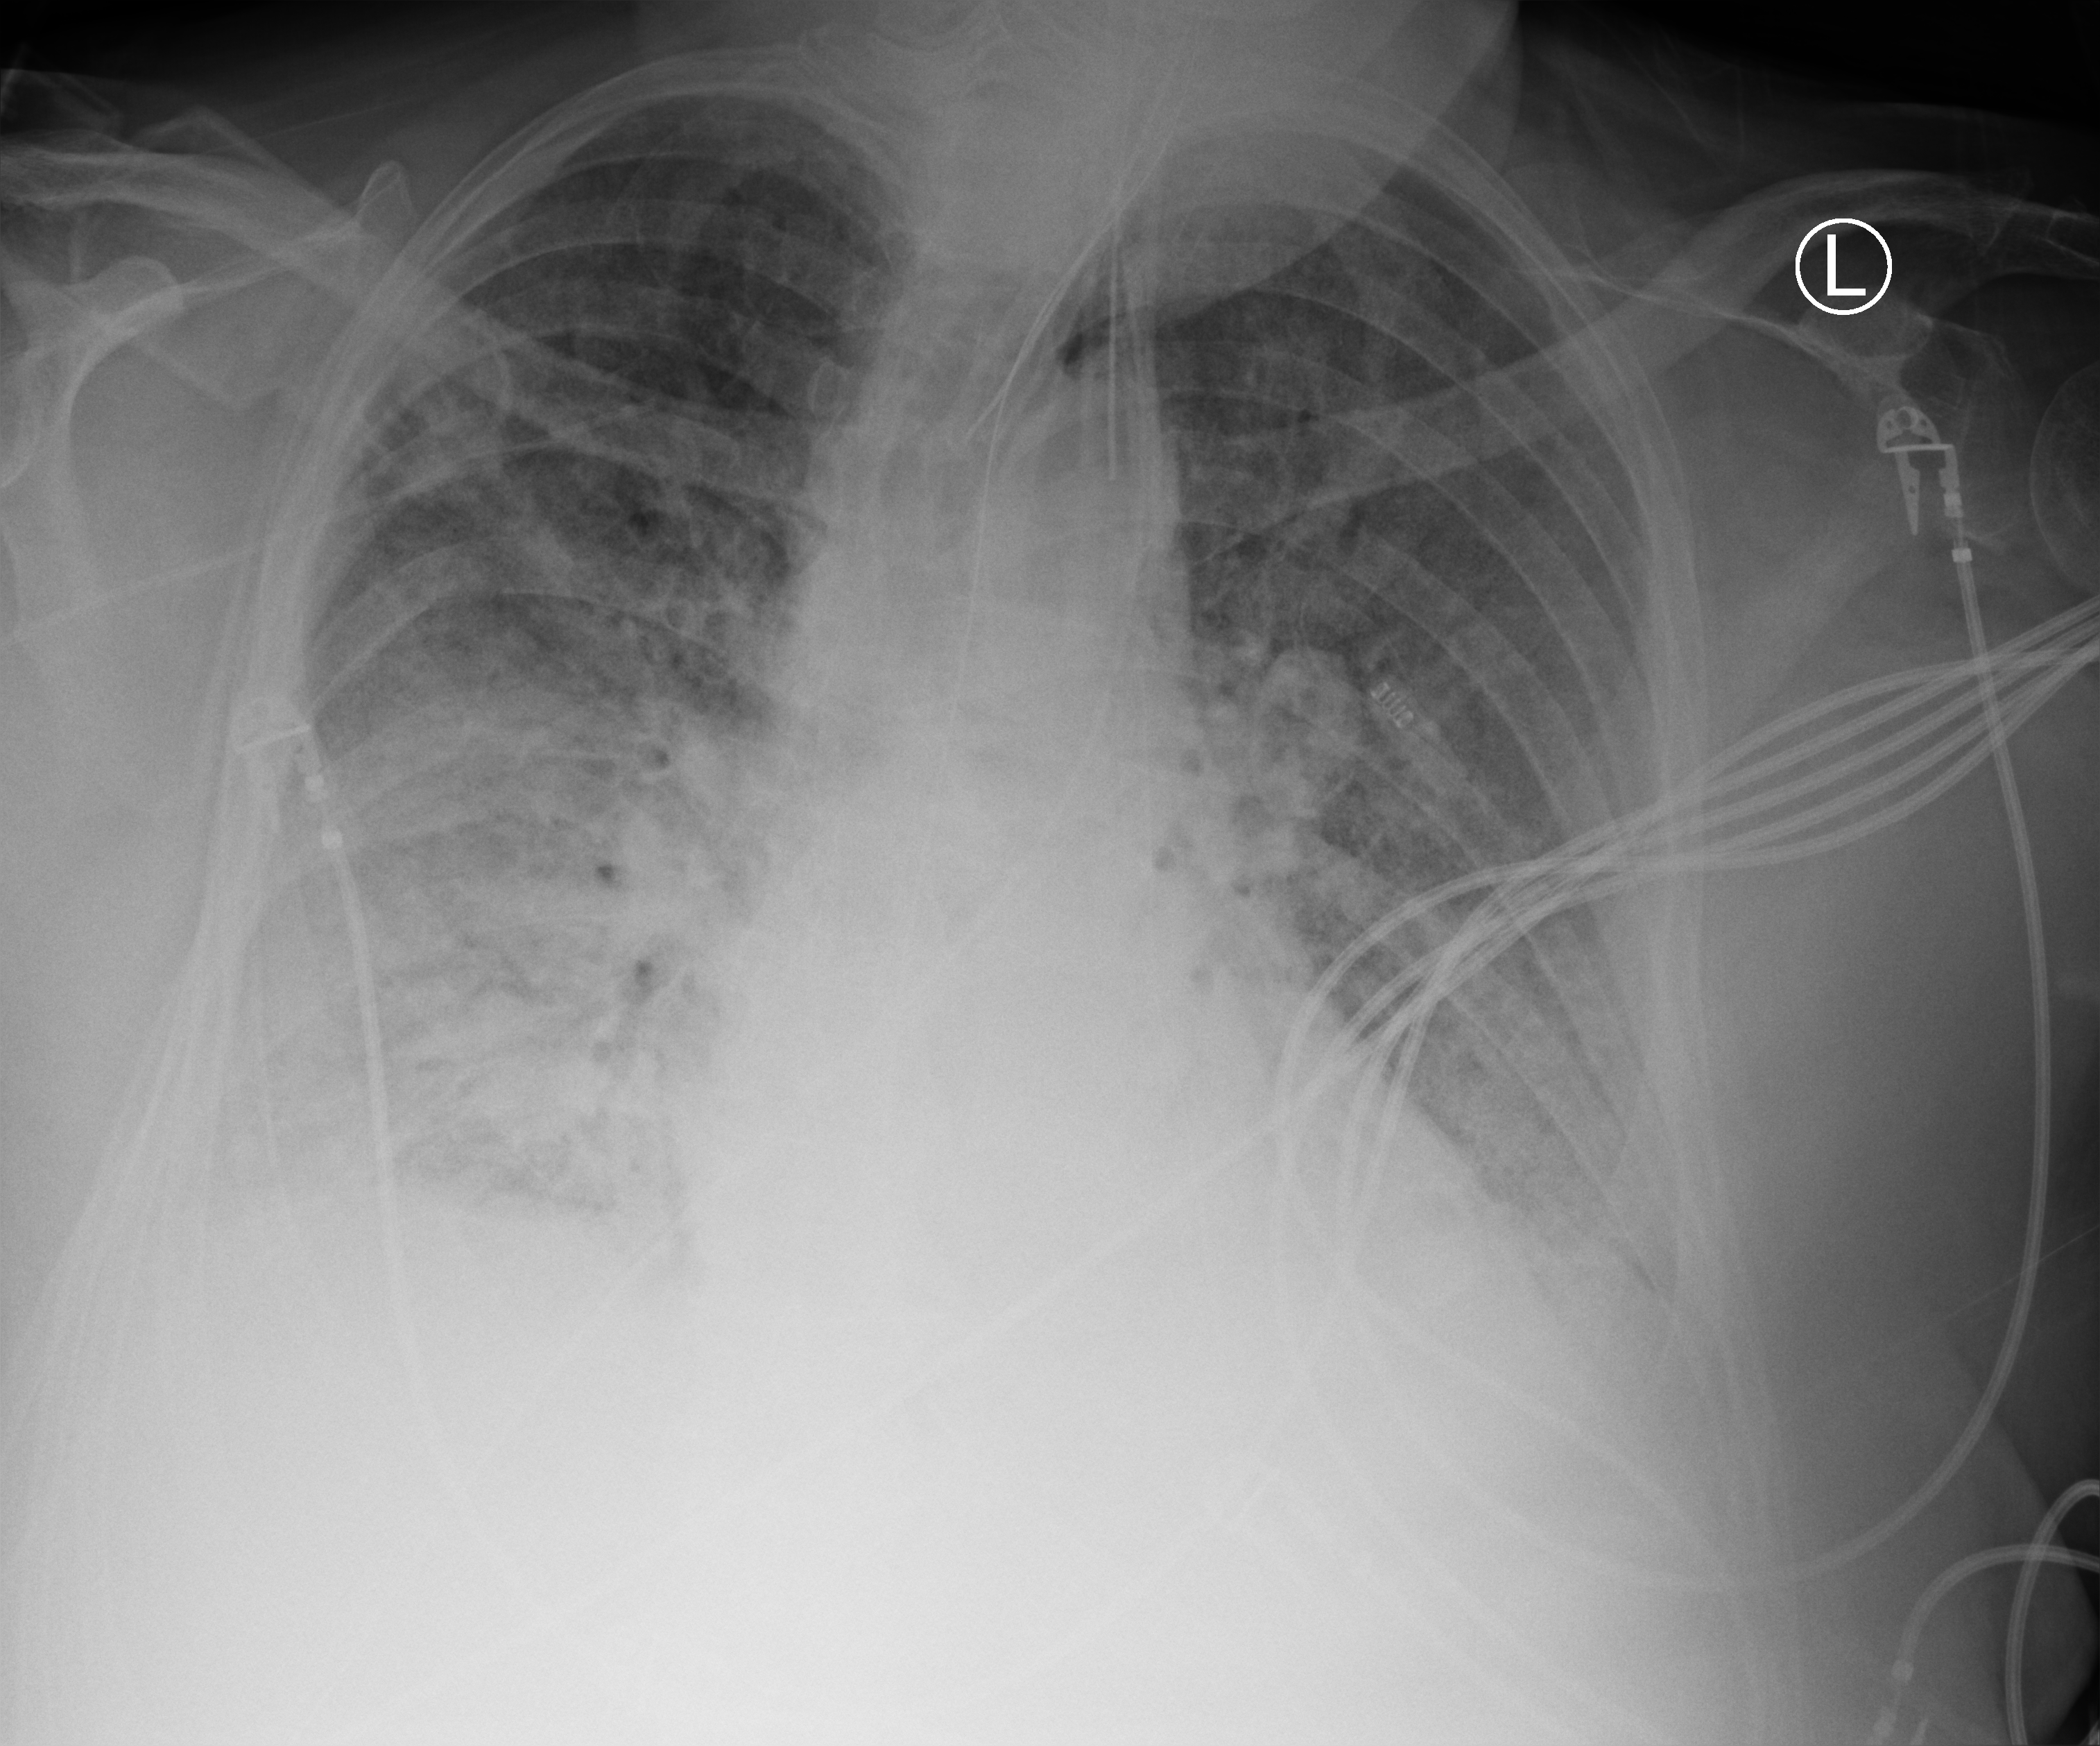
Chest X-ray (portable); anteroposterior (AP) projection. Patient hospitalised with COVID-19; male, aged 60–74 years.
Admission-level facts for this patient (not findings on this image; timing relative to this image not recorded): admitted to intensive care during this hospital stay: yes.